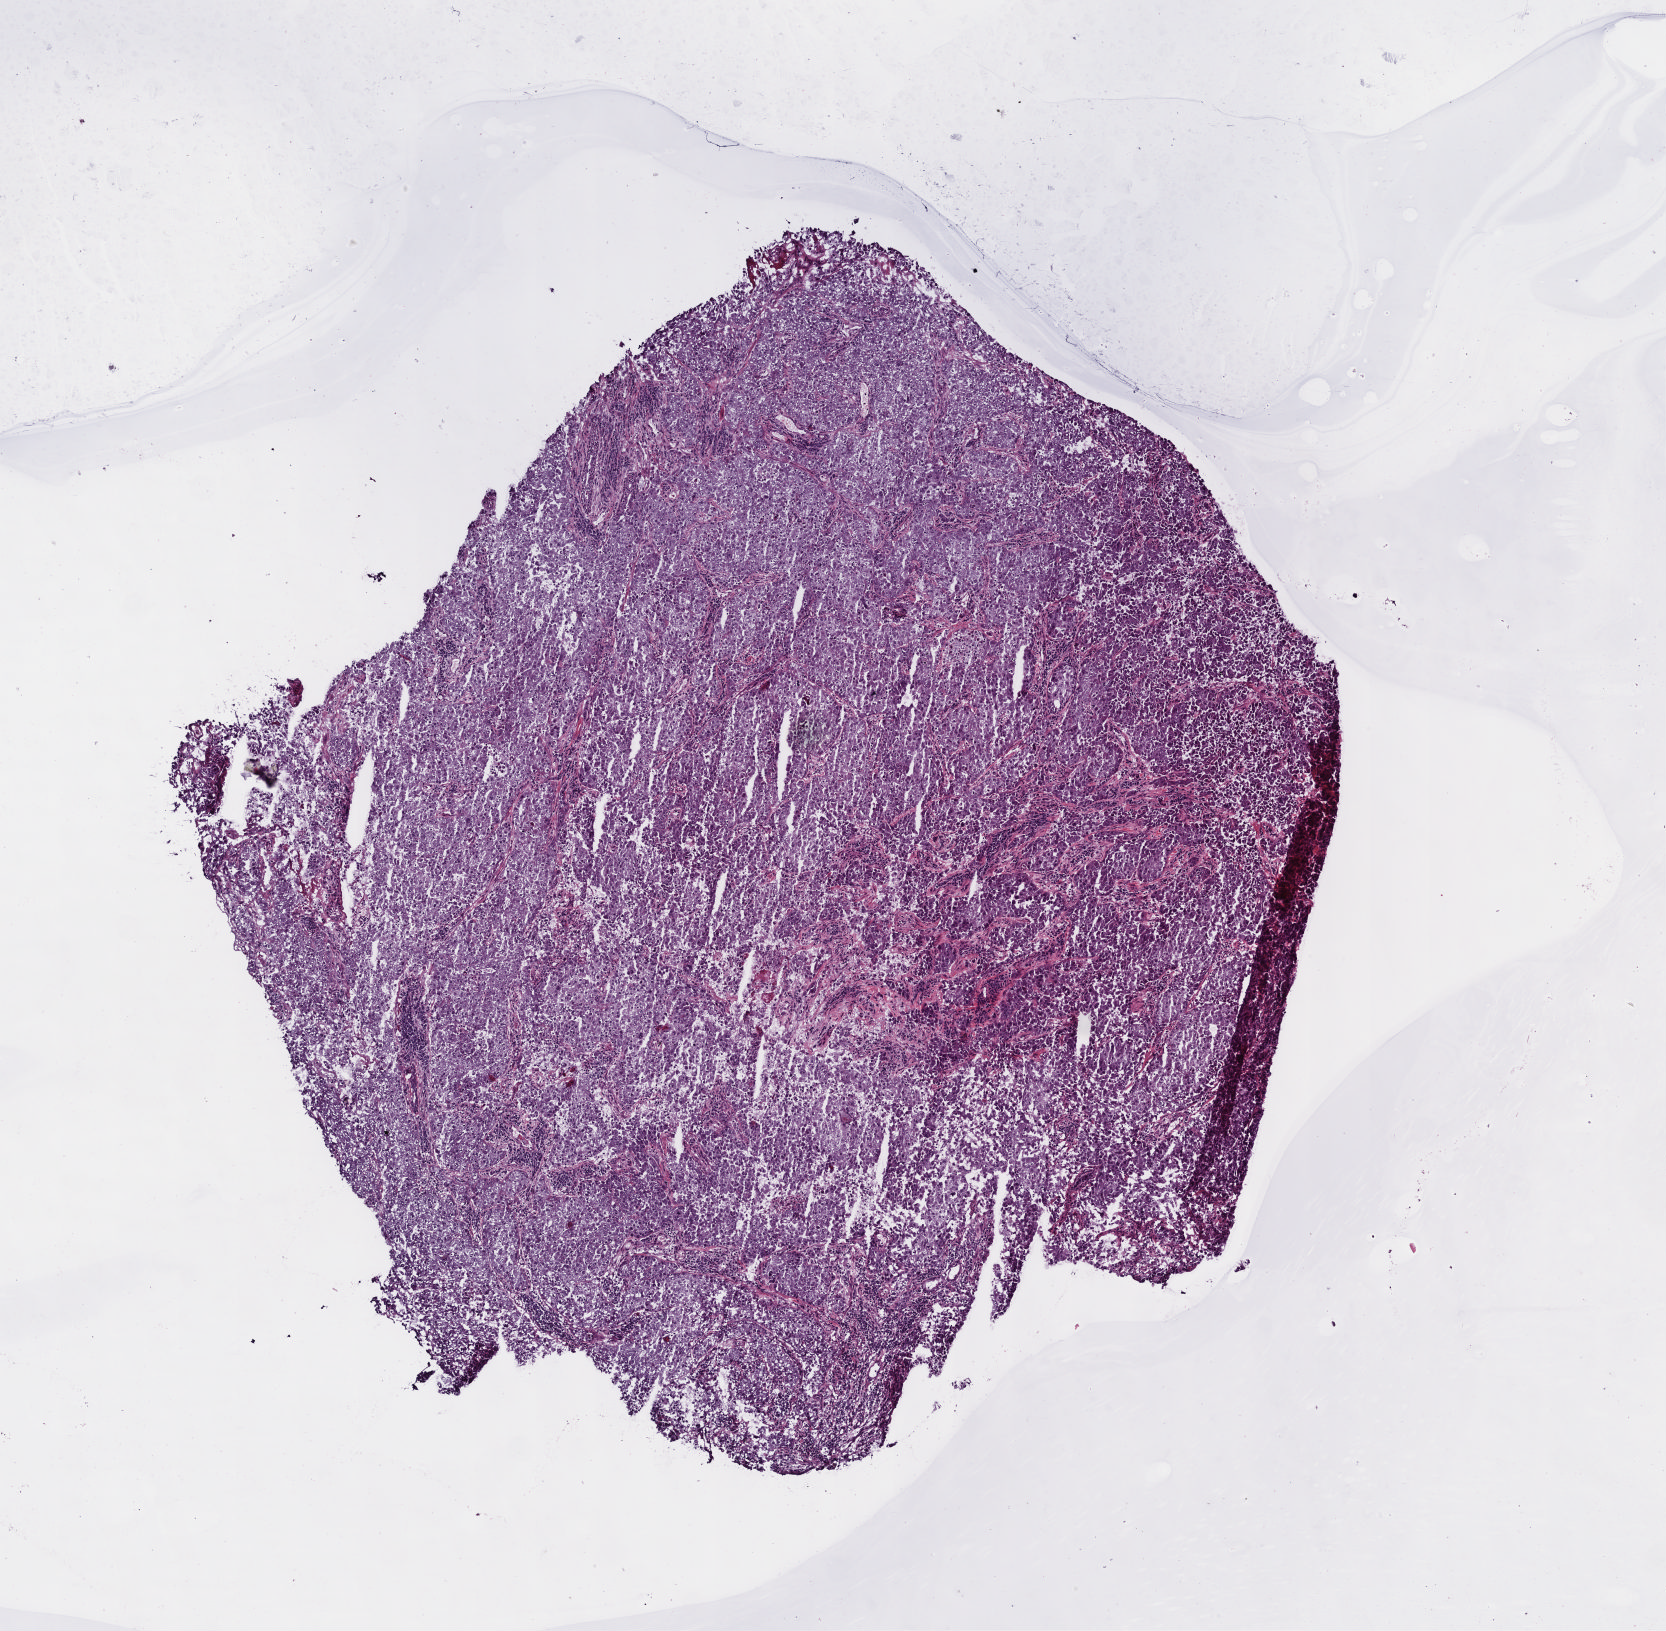
Whole-slide histology image, Hematoxylin and eosin (H&E) stained — shown as a low-resolution overview of the whole scanned area (about 6.5 x 6.4 mm). Frozen section. Primary tumour sample from the lung. Female patient; age at initial diagnosis 40 years. Pathologist review of this section (percent, as recorded): tumour cells 80%, tumour nuclei 90%, normal cells 0%, stromal cells 0%, necrosis 20%. Inflammatory infiltration, as recorded: lymphocyte infiltration 0%, monocyte infiltration 0%, neutrophil infiltration 0%.
Diagnosis: Adenocarcinoma, NOS (upper lobe, lung). AJCC pathologic stage: IV (7th edition).